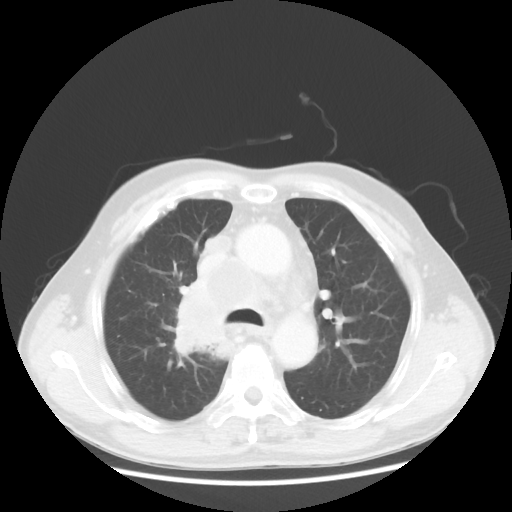
Chest CT, one axial slice. Position 82 of 124 along the scan axis. Lung window (W 1500 / L -600 HU). 5 mm slice thickness. 512 × 512 image matrix. Male patient, age 64 years. From the clinical record (not read from this slice): clinical TNM (as recorded): T3 N3 M0; histopathological grade: G3.
Outlined on this slice (bounding box drawn by a radiologist):
- lung tumour (recorded histology: small cell carcinoma): bounding box [x1, y1, x2, y2] px = [167, 277, 244, 380]